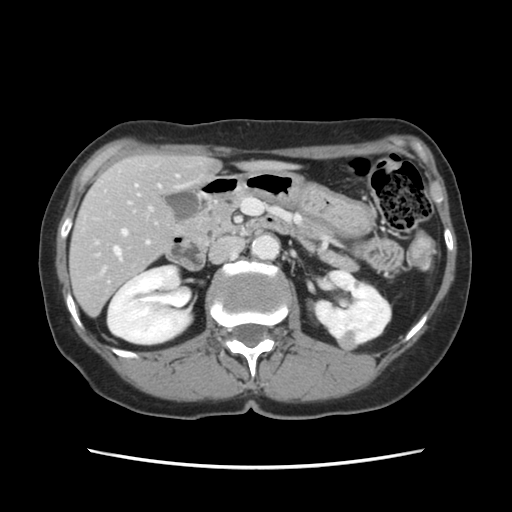
Contrast-enhanced abdominal CT, one axial slice. Slice 56 of 120 in the series (ordered by position). 120 kVp. Intravenous contrast given. Soft-tissue window (W 400 / L 40 HU). 2.5 mm slice thickness. 512 × 512 image matrix, field of view 330 × 330 mm. Female patient, age 70 years. Case-level facts recorded for this patient, not image findings: diagnosis: colorectal cancer liver metastases, imaged before liver resection; multiple liver metastases: no; largest metastasis: 2.5 cm; disease in both lobes: no.
Outlined on this slice (manually delineated by an expert):
- hepatic veins: box from (x=114, y=248) to (x=121, y=258) px
- liver: (x=70, y=155)–(x=217, y=314)
- planned liver remnant (the part of the liver to remain after resection): (x=71, y=155)–(x=217, y=305)
- portal vein (with intrahepatic branches): (x=96, y=175)–(x=178, y=244)